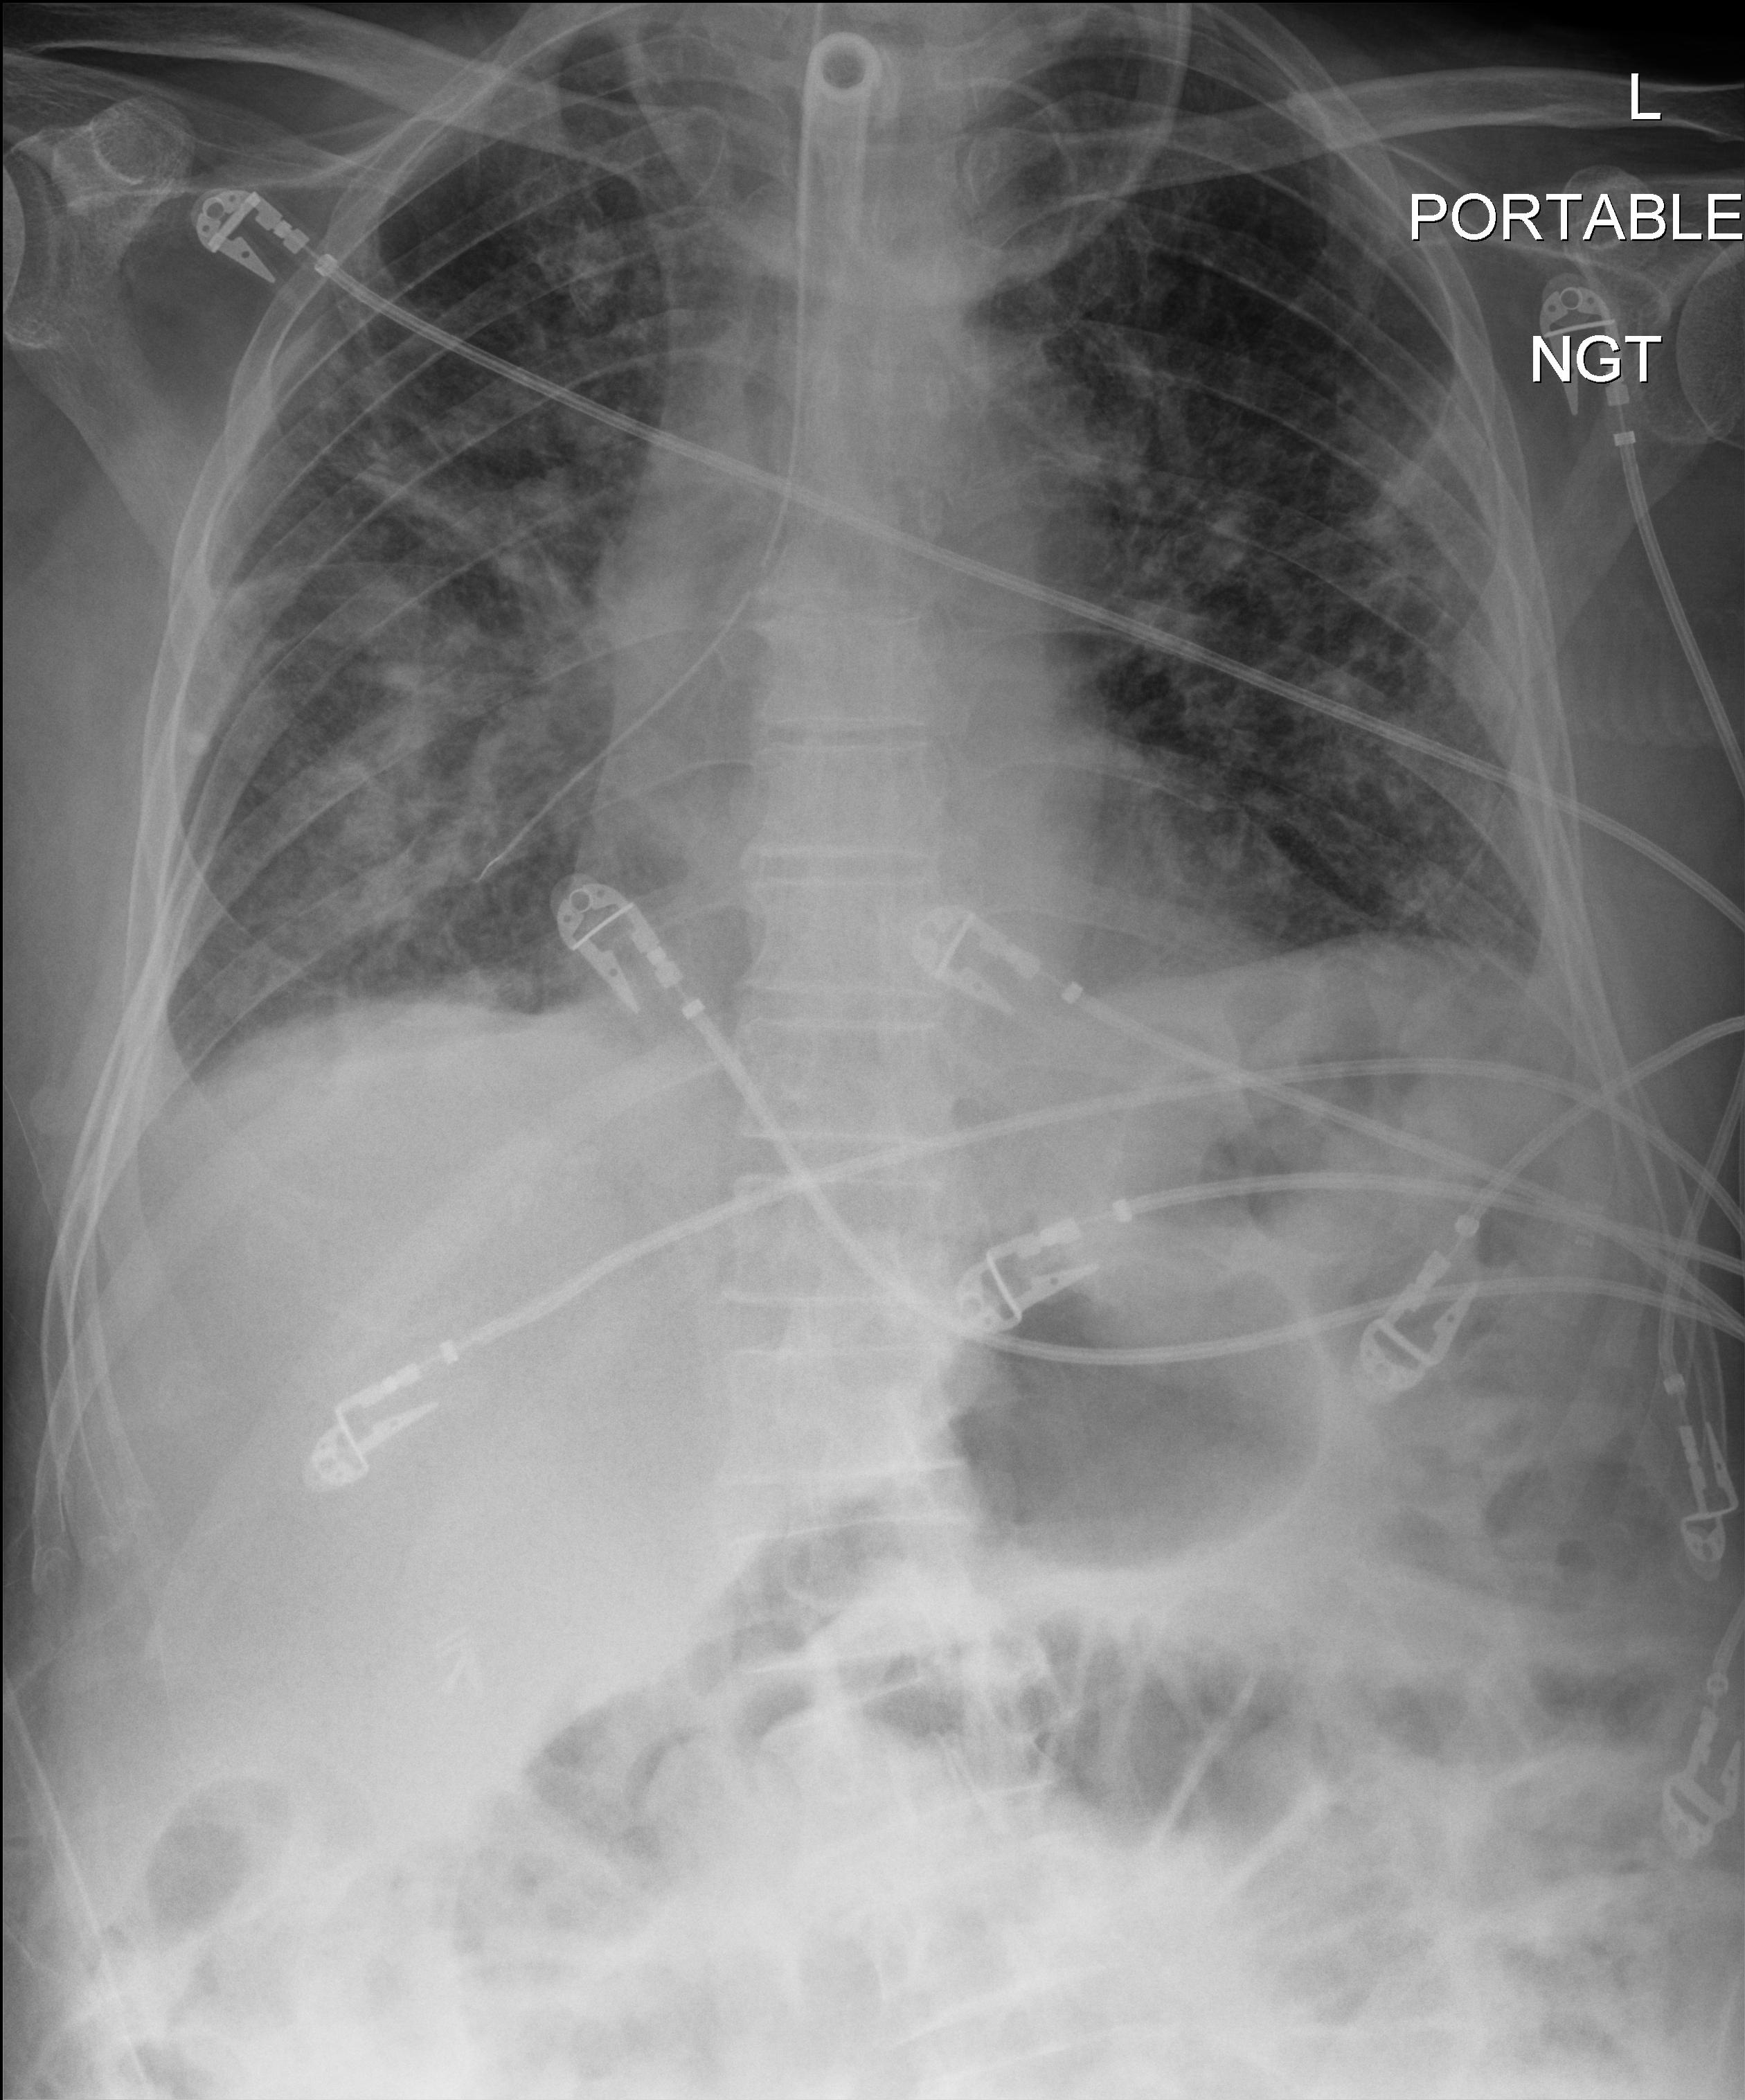
Chest radiograph. Male patient hospitalised with COVID-19, age 75–90 years.
Admission-level facts for this patient (not findings on this image; timing relative to this image not recorded): admitted to intensive care during this hospital stay: yes.